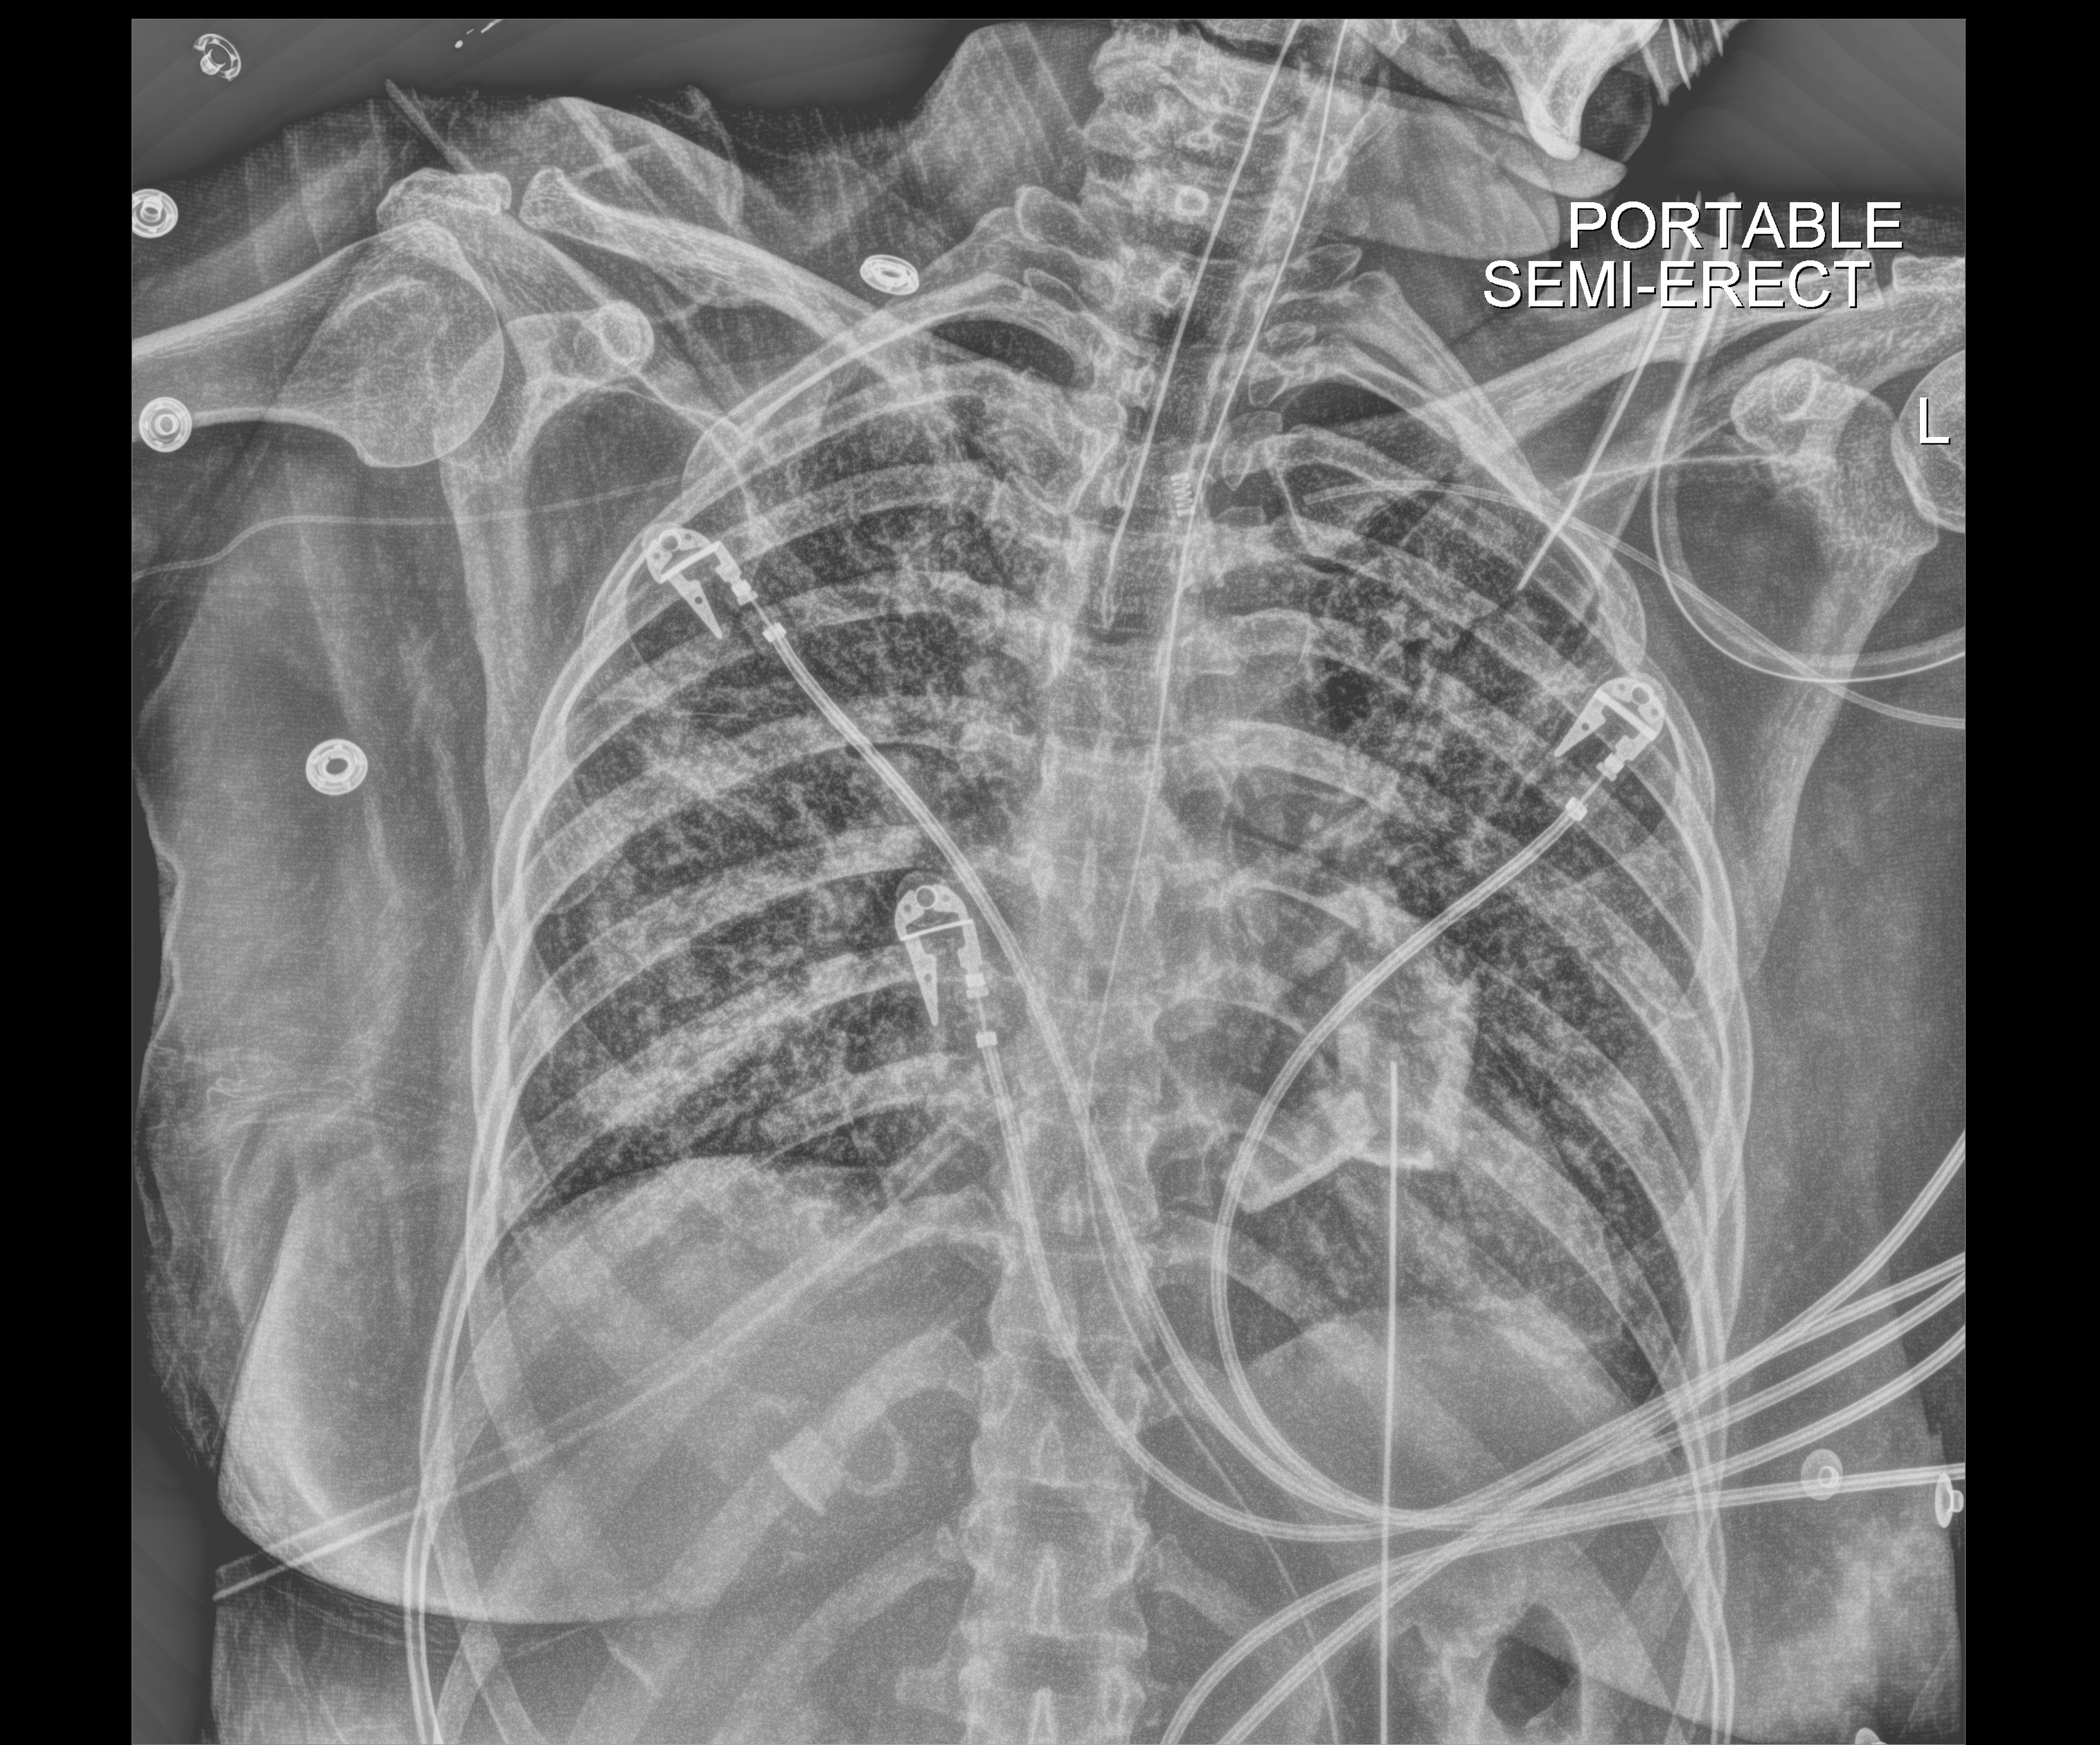
Chest X-ray (portable). Male patient hospitalised with COVID-19, age 18–59 years.
Hospital-stay facts (about this admission, not read from this image; timing relative to this image not recorded): other chronic lung disease (admission record): no; admitted to intensive care during this hospital stay: yes; mechanically ventilated during this hospital stay: yes.